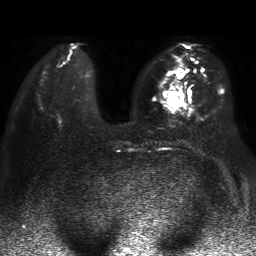
Breast MRI, one axial slice. Position 17 of 50 along the scan axis. Diffusion-weighted series; image 2 of 4 stored at this slice position (different b-values; order by instance number). 1.5 T. 4 mm slice thickness. 256 × 256 image matrix. Female patient.
Annotated regions visible in this slice (manually delineated by an expert):
- tumour on diffusion-weighted imaging: bounding box [x1, y1, x2, y2] px = [168, 93, 184, 107]